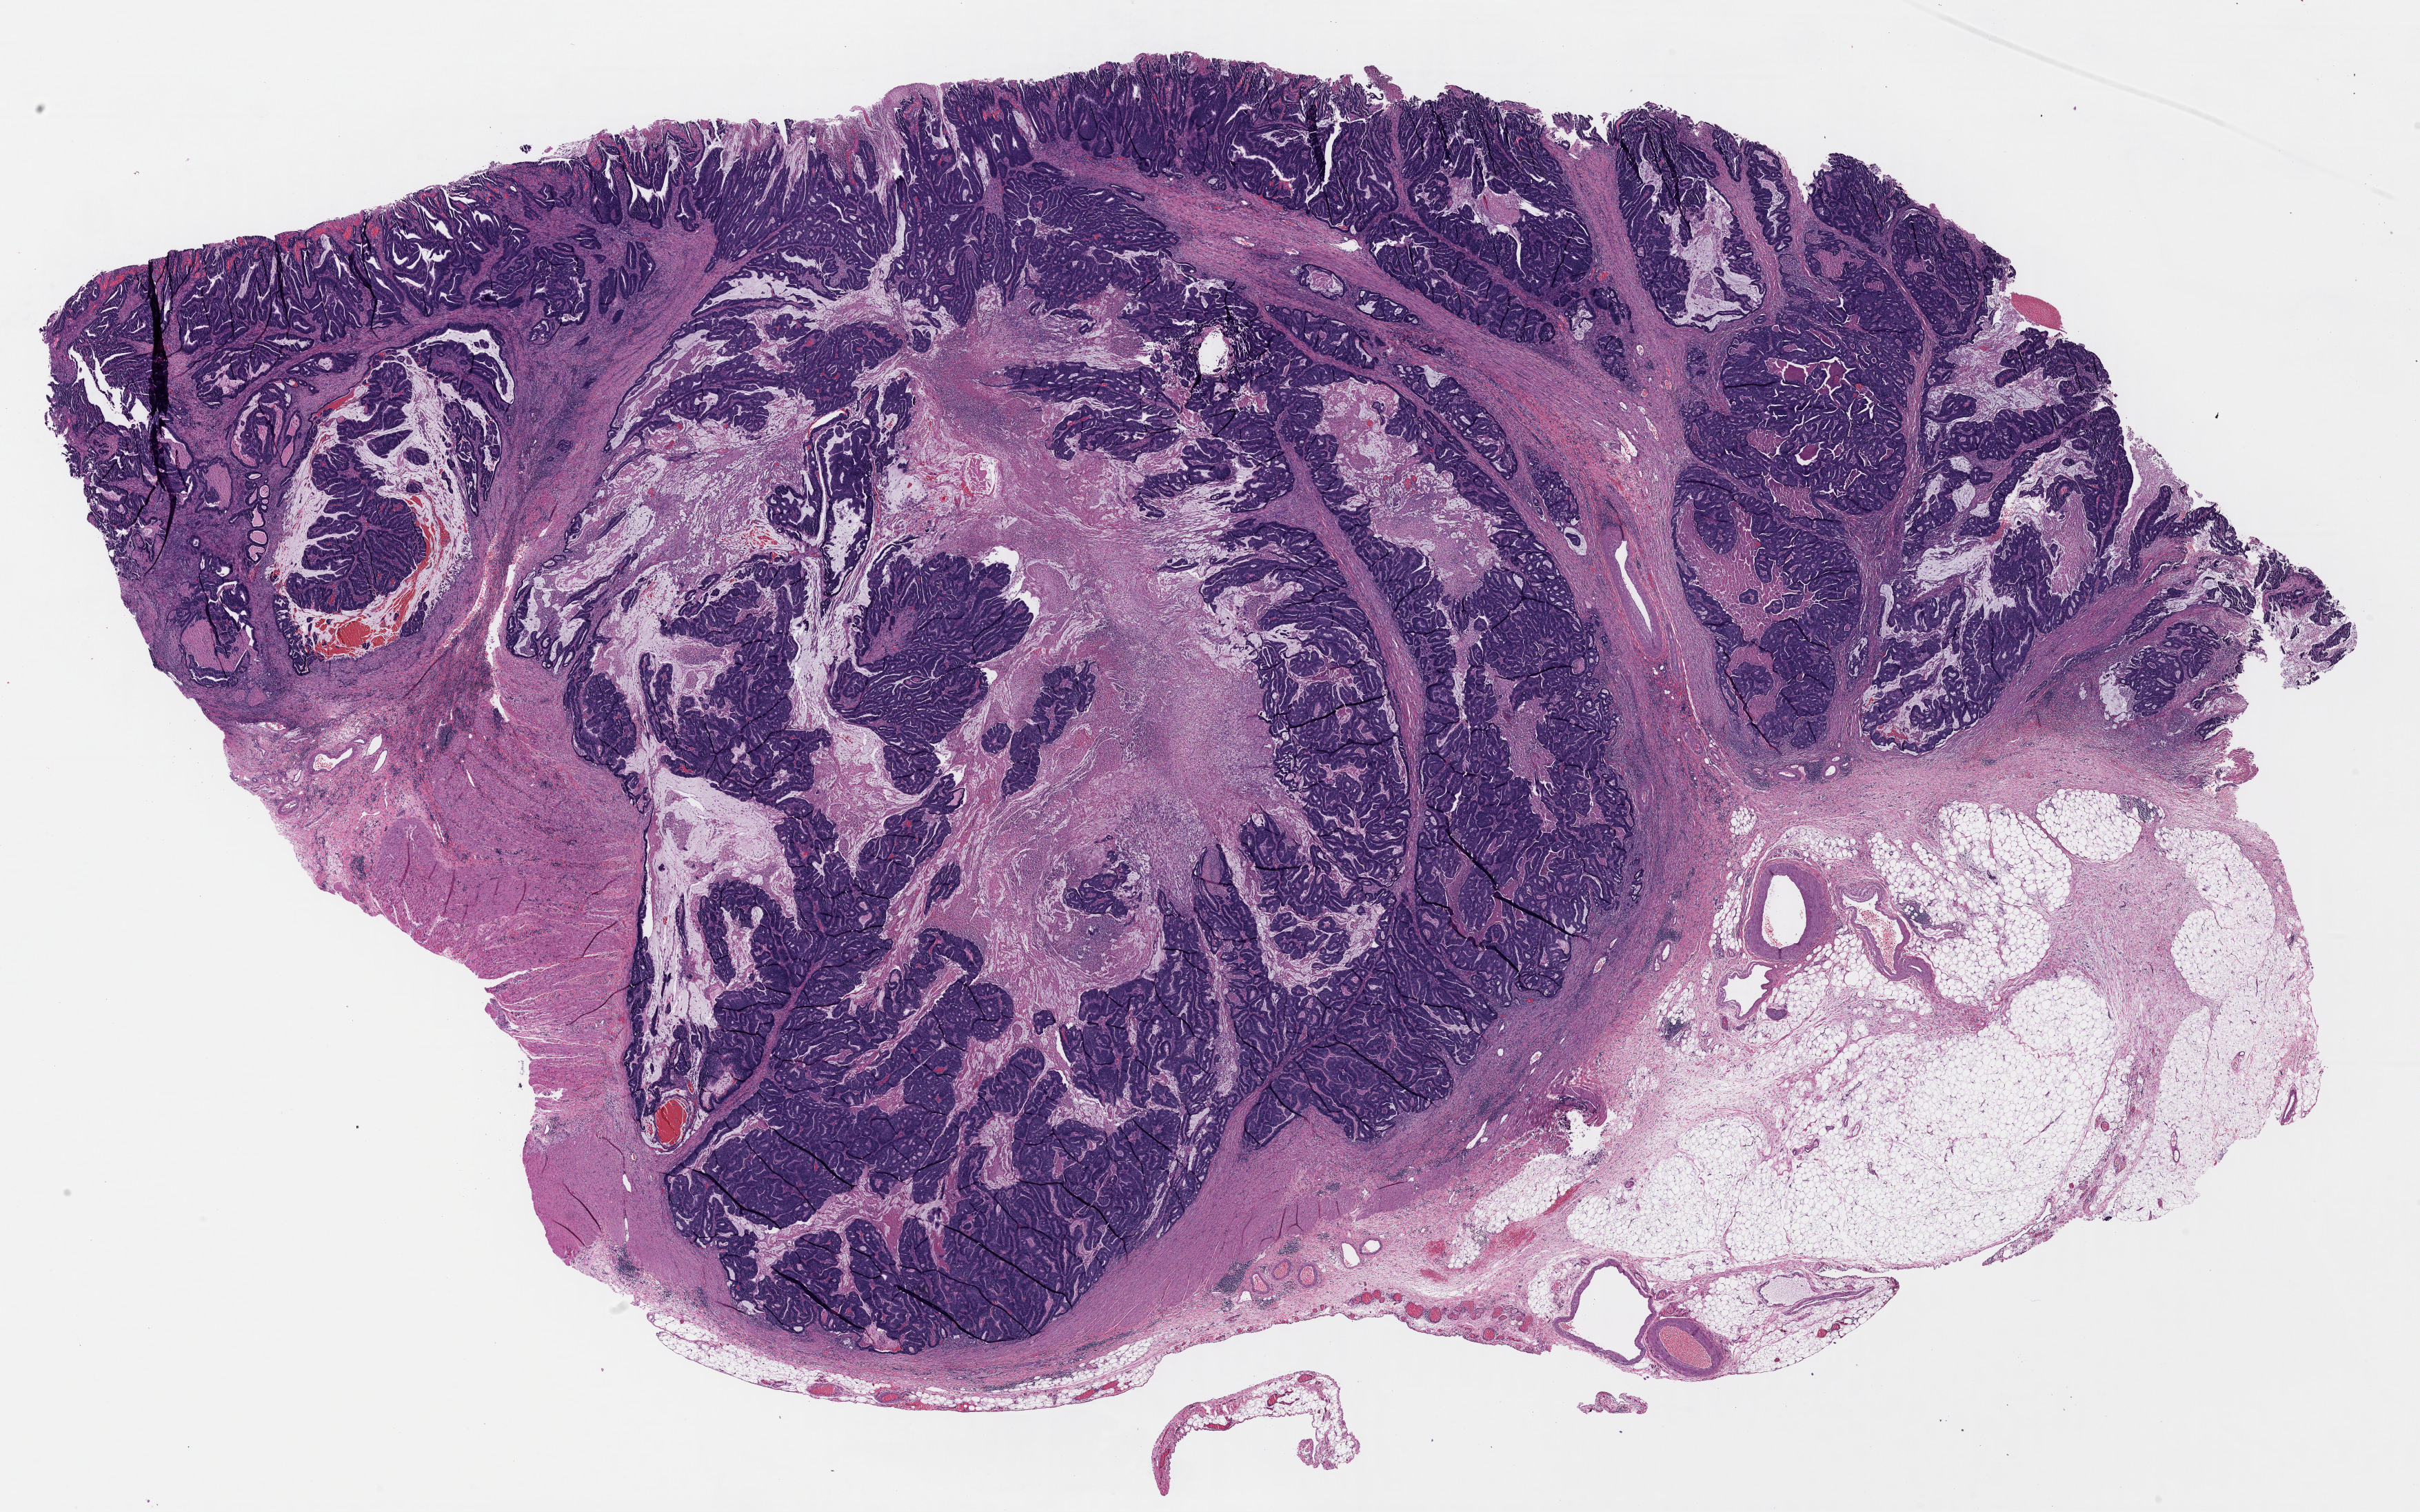
Whole-slide histology image, H&E-stained — low-resolution overview of the scanned area, about 27.6 x 17.2 mm. FFPE section. Colon, primary tumour sample. Patient sex: female.
Lymph nodes positive (case pathology): 0 of 12 examined. AJCC pathologic stage: IIA (7th edition). Diagnosis: Adenocarcinoma, NOS (transverse colon).